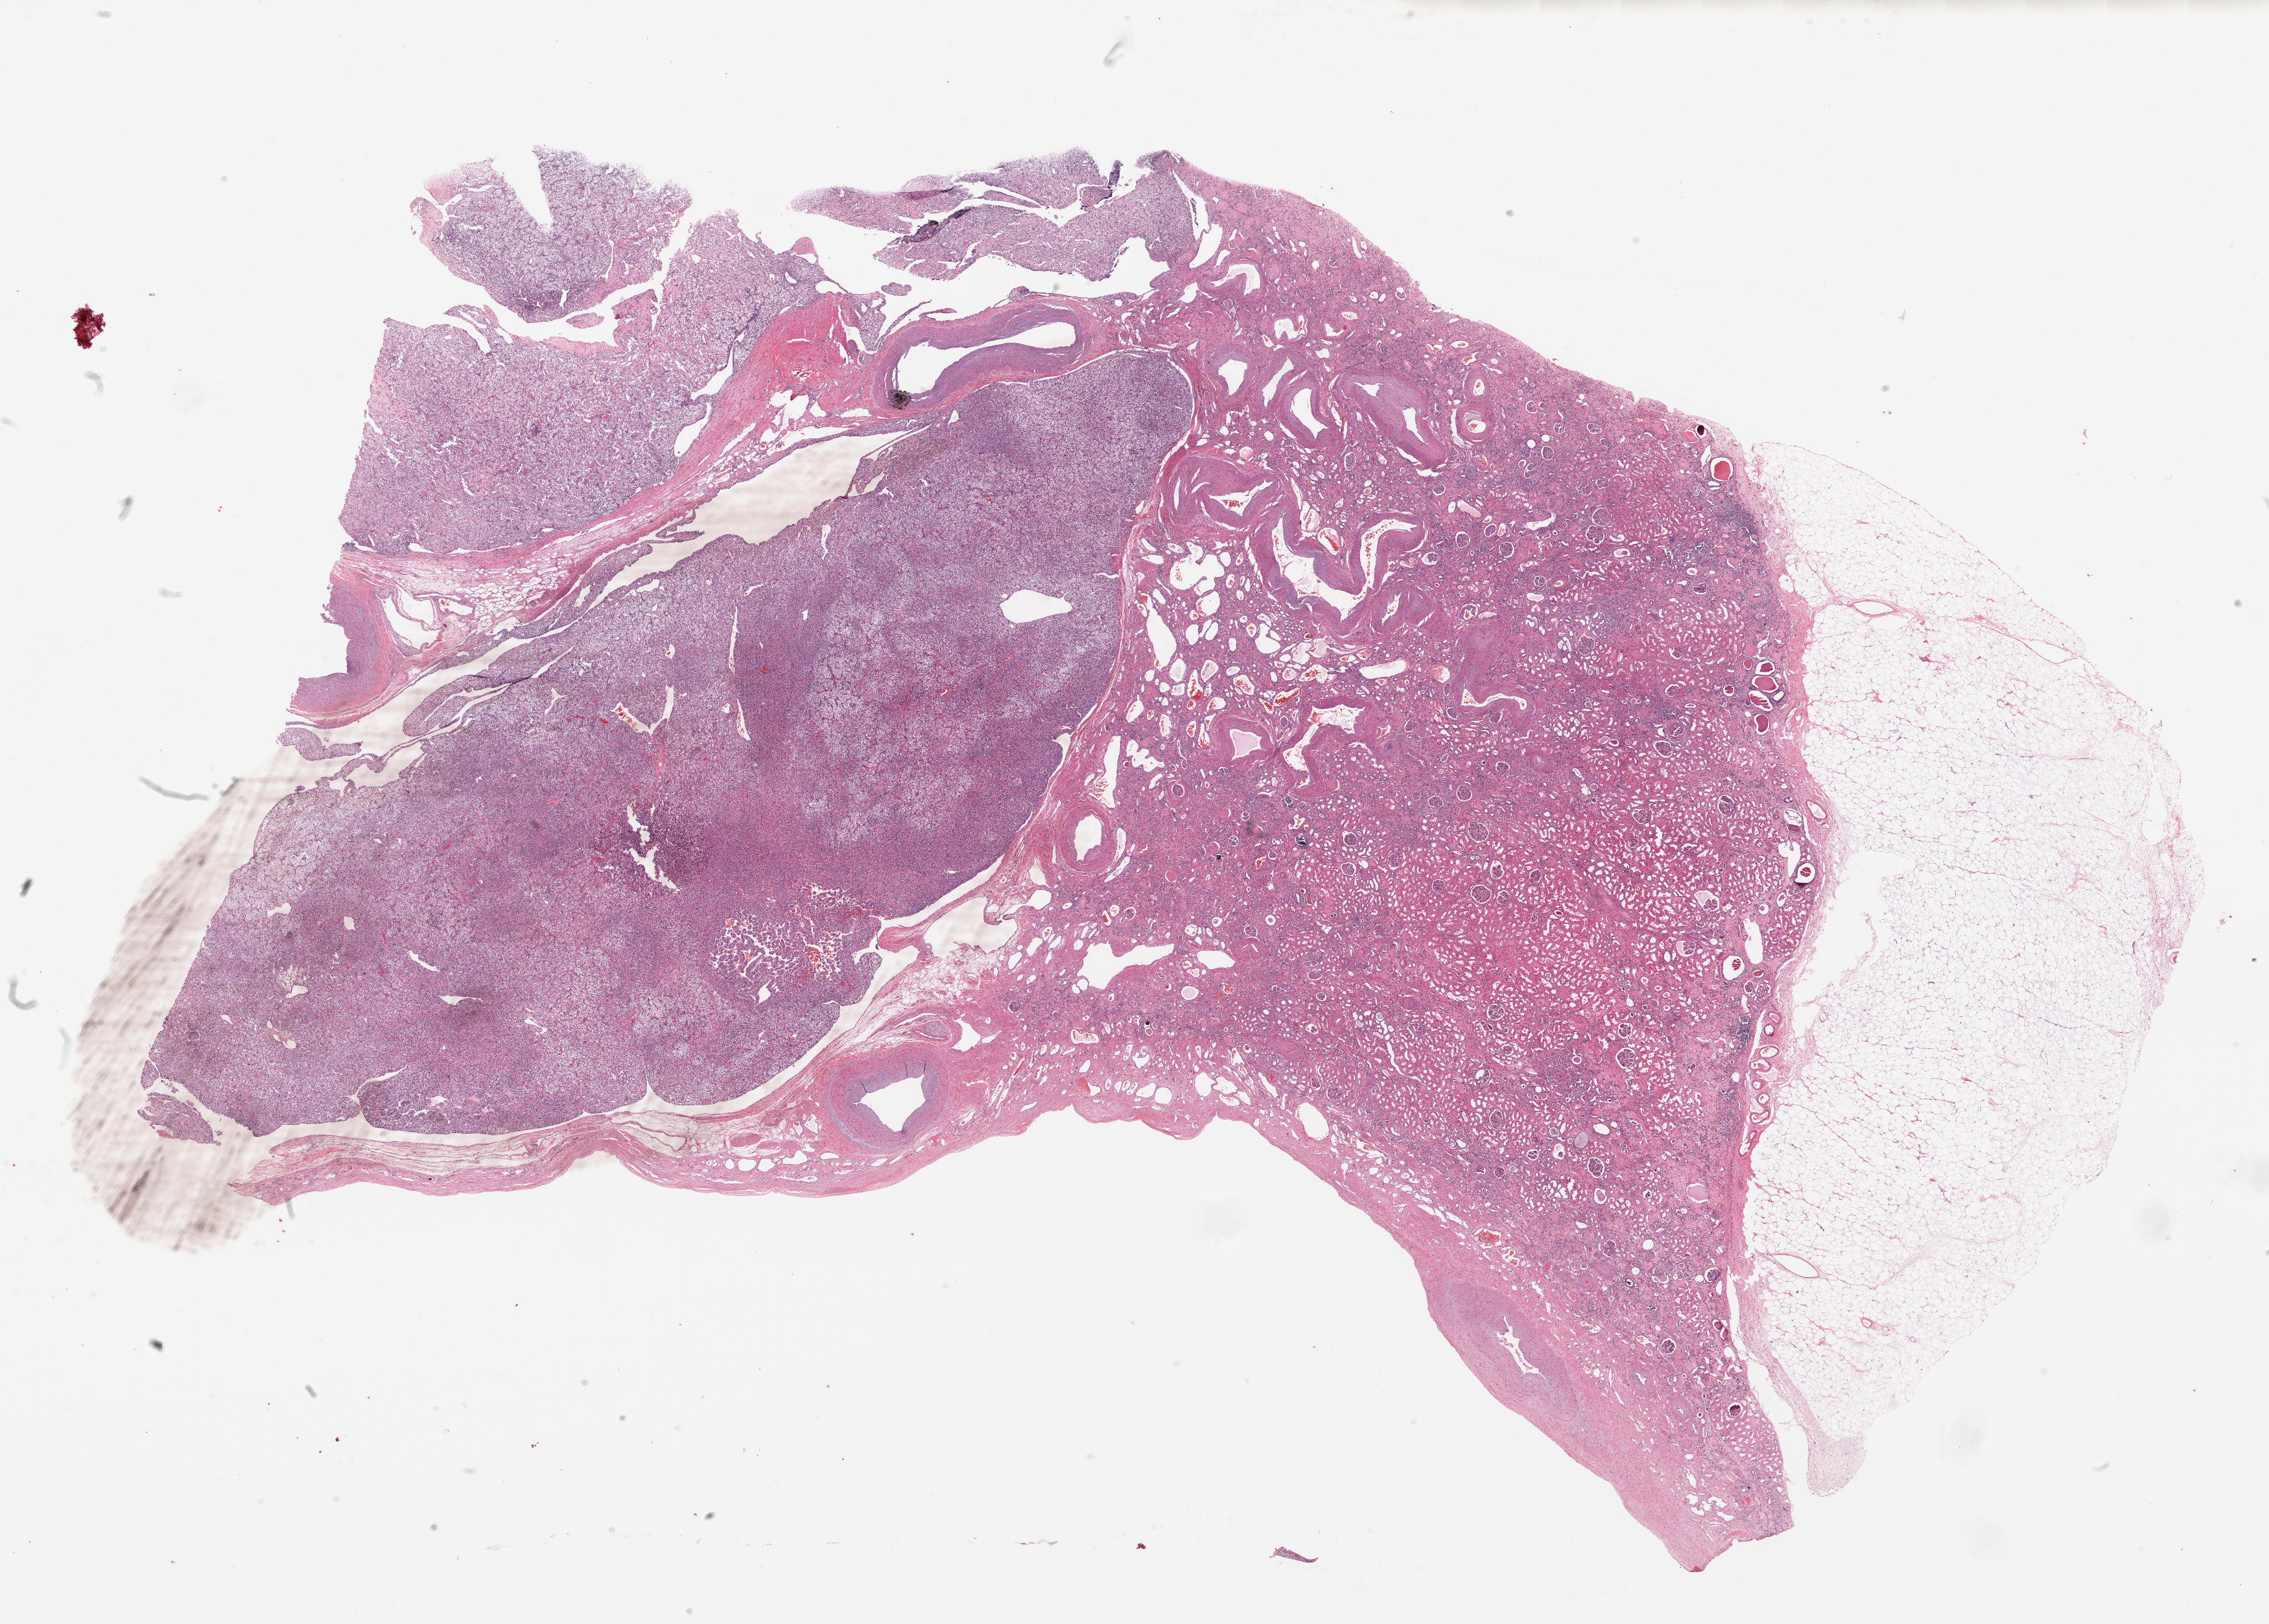
Hematoxylin and eosin (H&E) stained whole-slide image — shown as a low-resolution overview of the whole scanned area (about 28.1 x 20.1 mm); formalin-fixed paraffin-embedded (FFPE) diagnostic section; kidney, primary tumour sample. Male patient.
Histologic diagnosis: Clear cell adenocarcinoma, NOS.